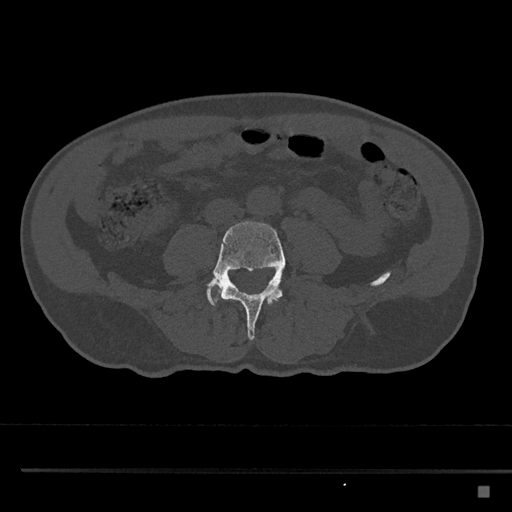
CT including the spine, one axial slice; slice 634 of 797 in the series (ordered by position); reconstruction kernel Br40s/3; 120 kVp; bone window (W 1800 / L 400 HU); 0.5 mm slice thickness; 512 × 512 image matrix, field of view 391 × 391 mm. Patient: male, 59 years. Case-level facts recorded for this patient, not image findings: primary cancer: prostate.
Outlined on this slice (semi-automatically segmented with operator editing):
- L3 vertebra: bounding box (x1, y1, x2, y2) in pixels: (225, 297, 281, 300)
- L4 vertebra: (209, 221, 286, 341)
- L5 vertebra: (207, 275, 217, 307)